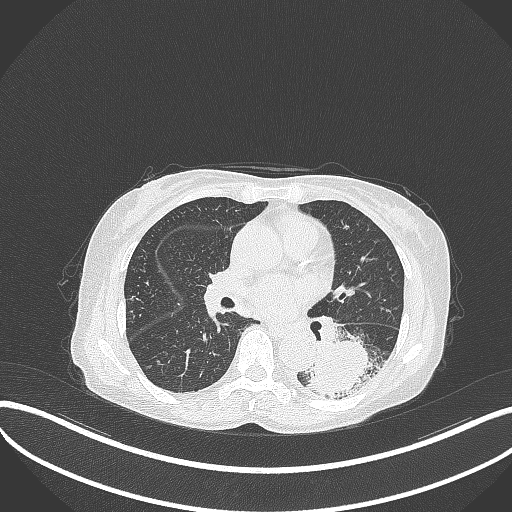
Chest CT, one axial slice; reconstruction kernel B70f; 120 kVp; lung window (W 1500 / L -600 HU); 1 mm slice thickness; 512 × 512 image matrix. Female patient, age 78 years. From the clinical record (not read from this slice): clinical TNM (as recorded): T3 N0 M1.
Structures marked on this image (rectangle marked by the reading radiologist):
- lung tumour (recorded histology: squamous cell carcinoma): bounding box [x1, y1, x2, y2] px = [305, 336, 385, 398]